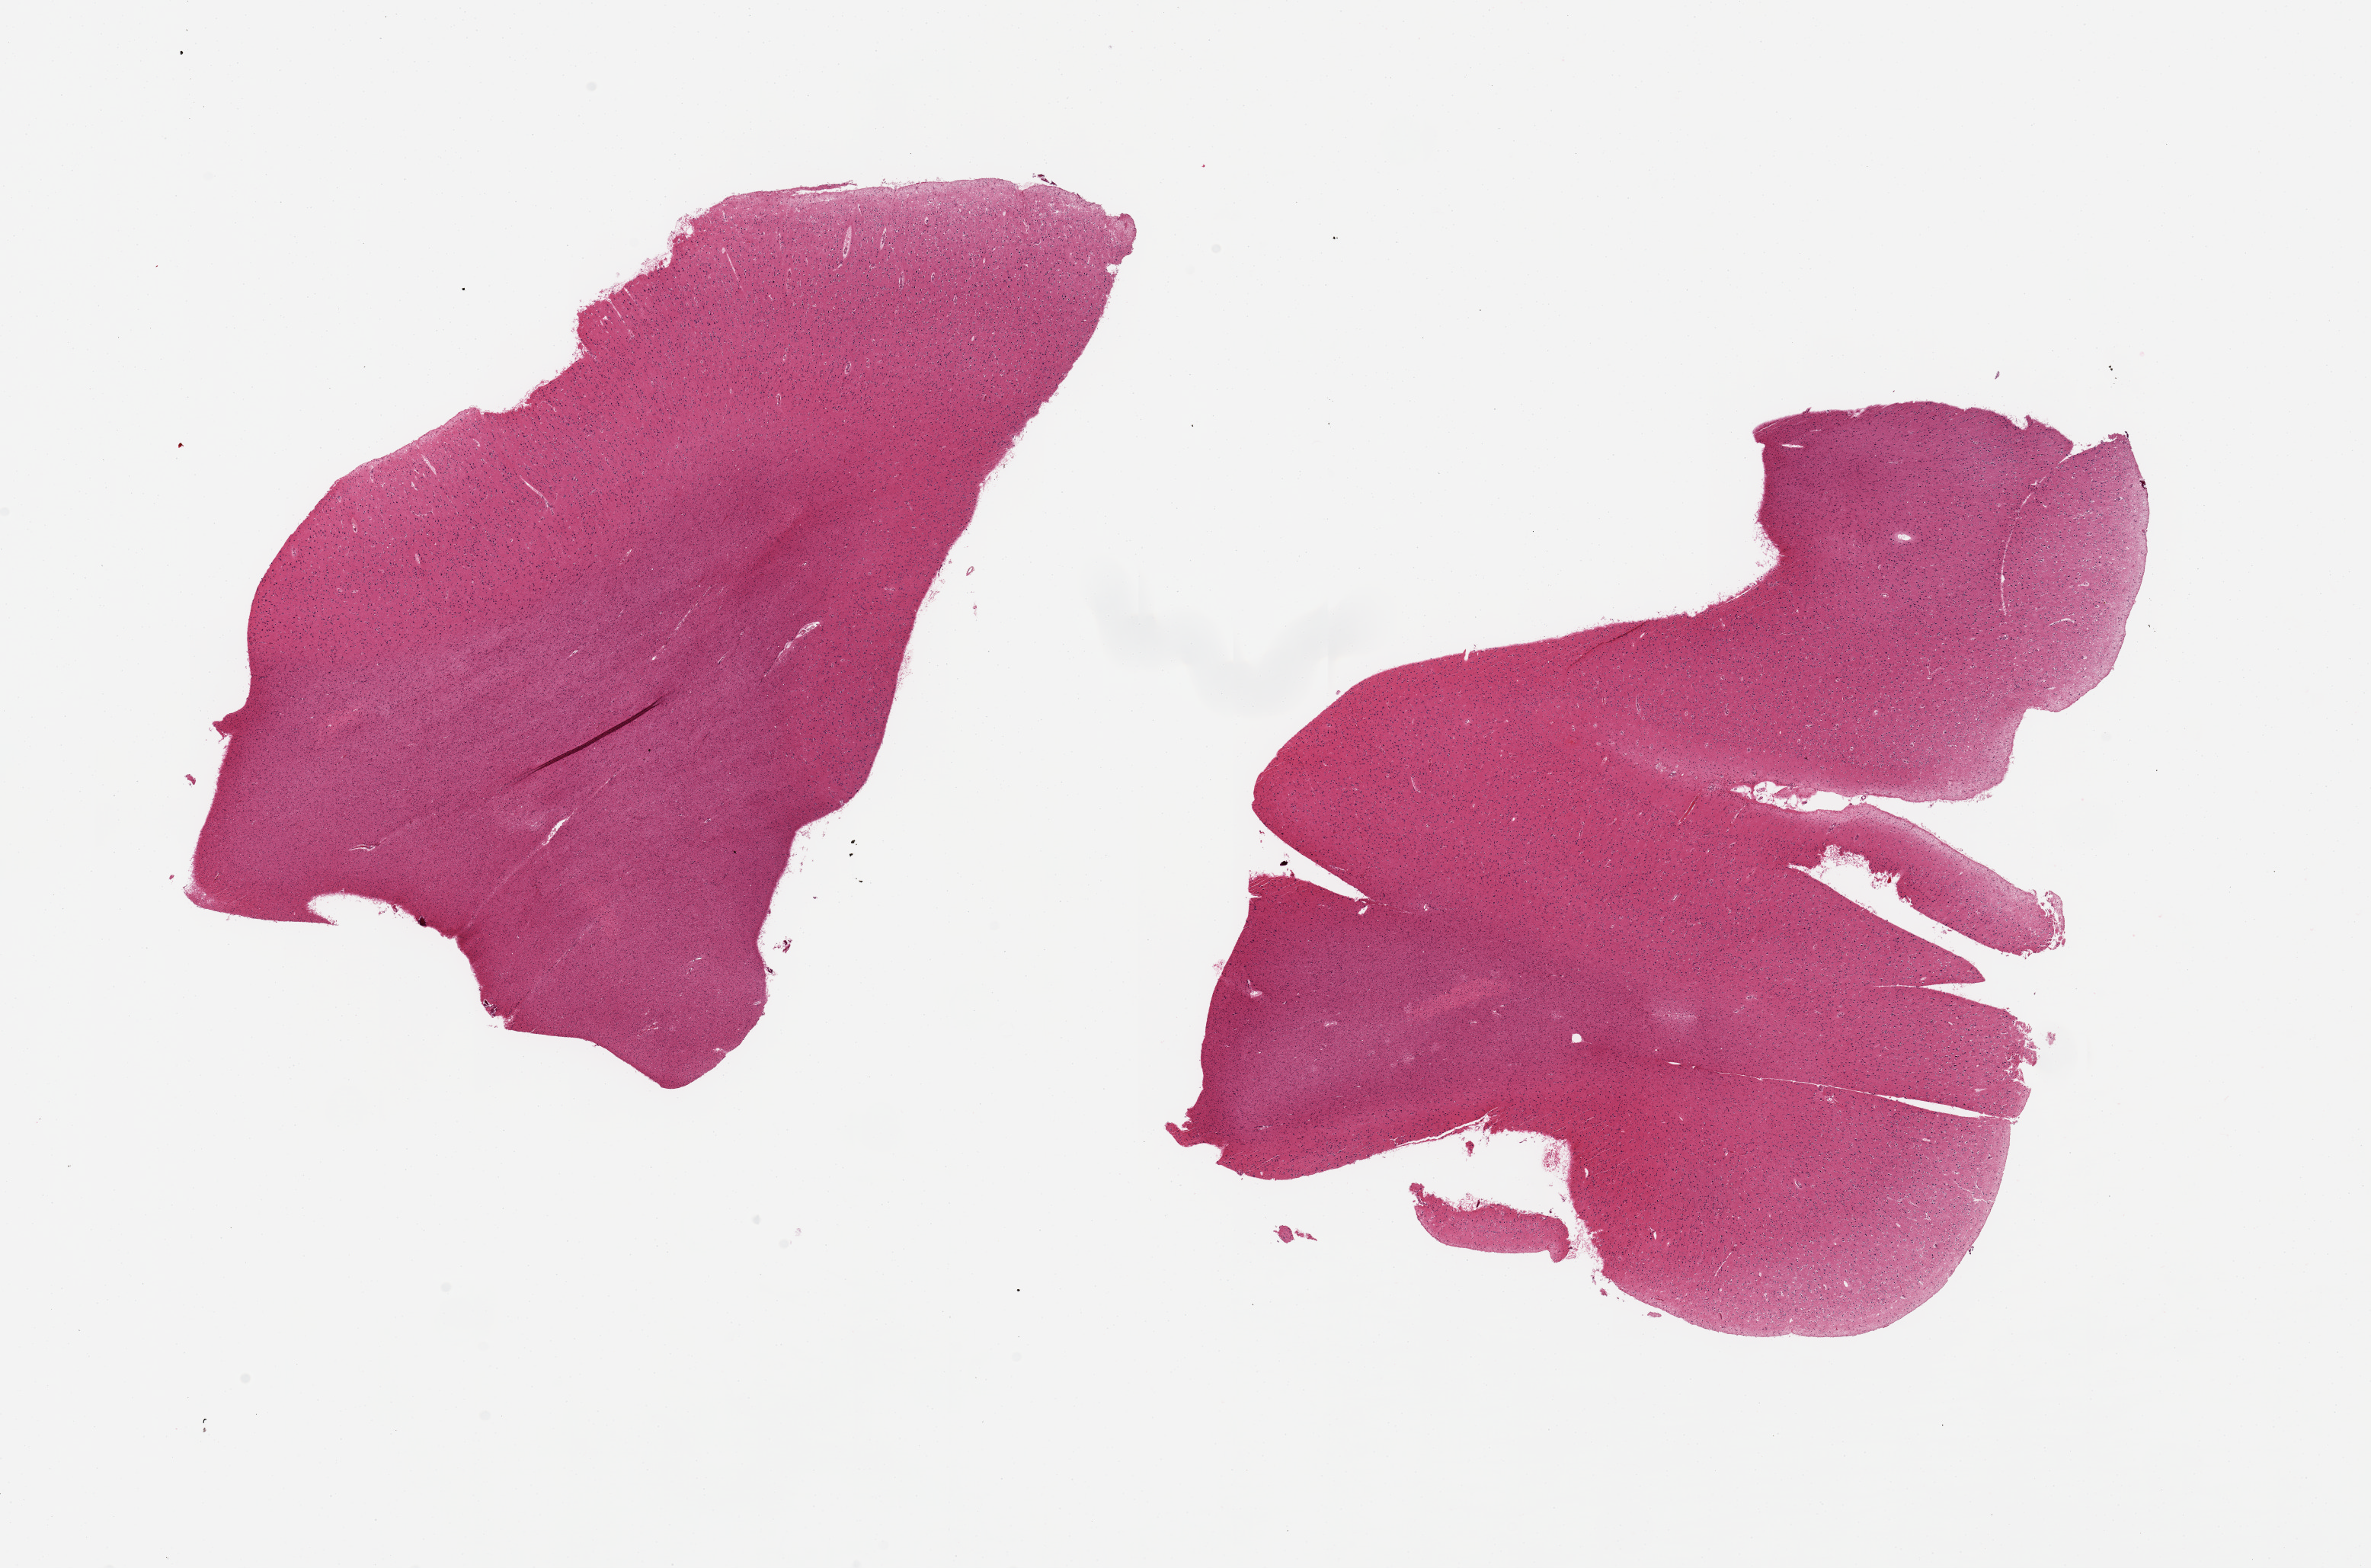
Whole-slide image, hematoxylin and eosin (H&E) stain — low-resolution overview of the scanned area, about 24.6 x 16.3 mm (acquisition: 20x scan), PAXgene-fixed paraffin-embedded (PFPE) section, section of cerebral cortex (target tissue), tissue donor sample.
• pathologist's review note for this sample: 2 pieces